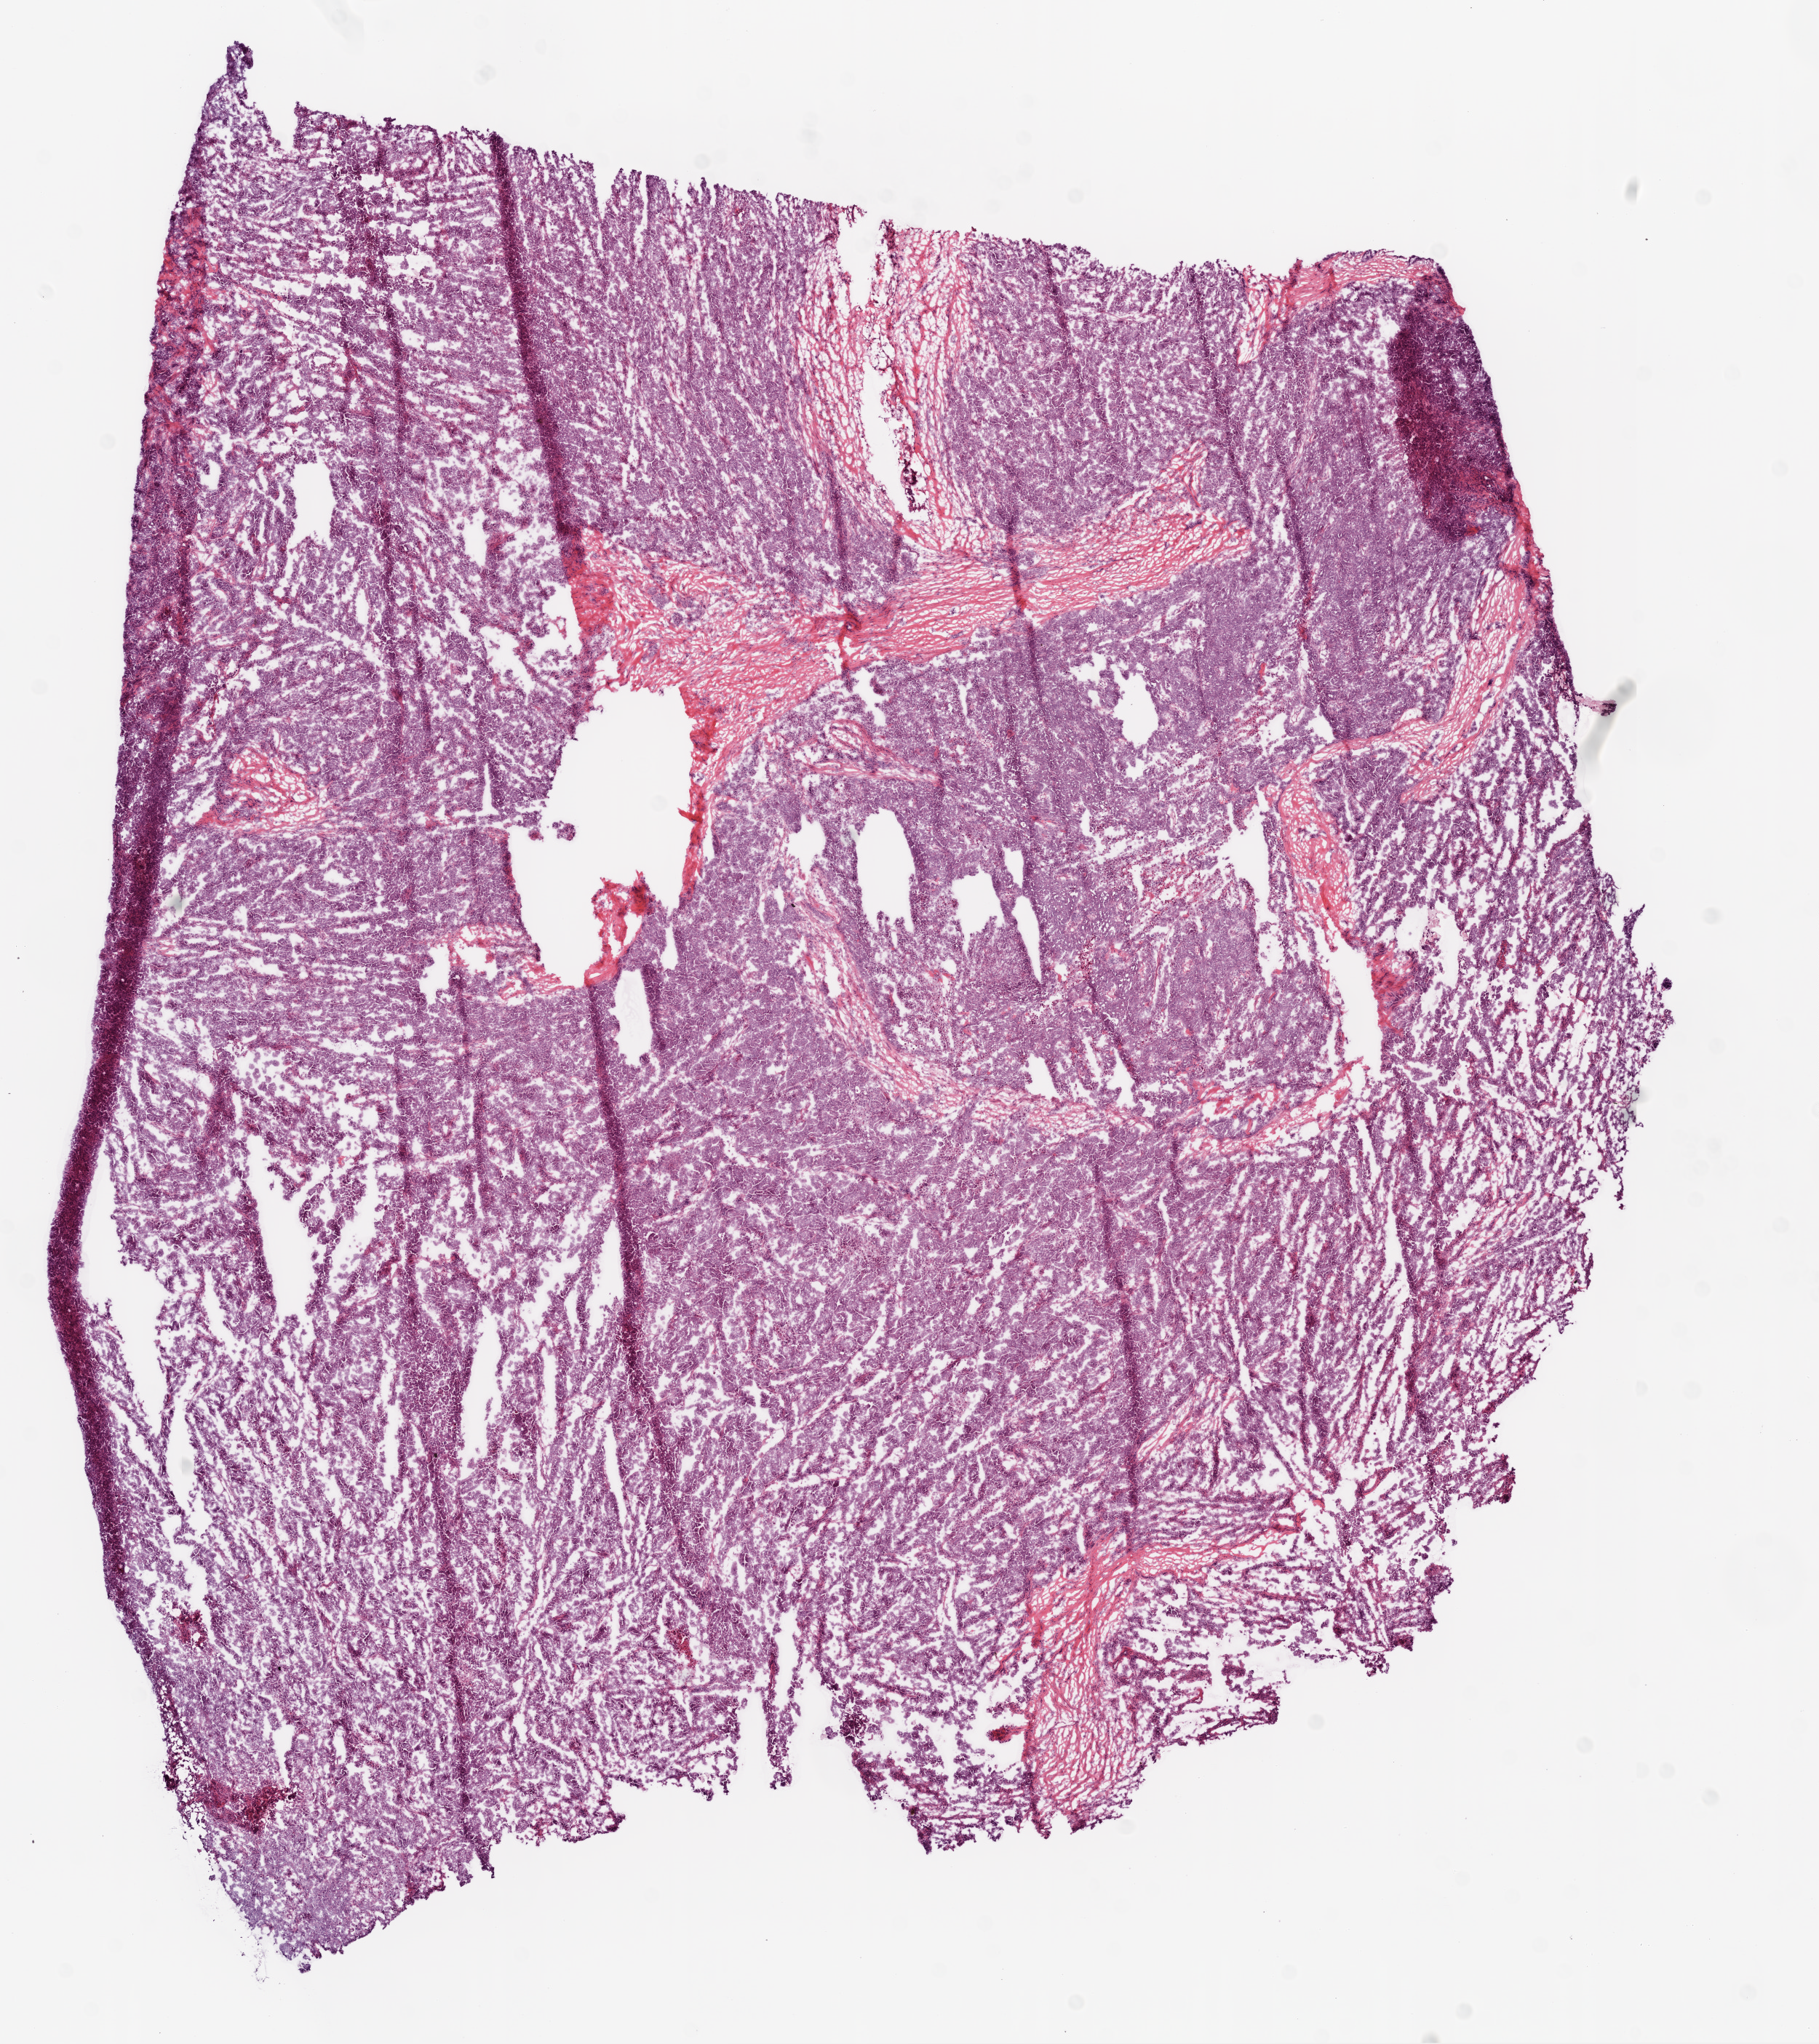
H&E-stained whole-slide image, low-resolution overview of the scanned area, about 10.0 x 11.3 mm. Frozen section from the bottom of the tissue portion. Sample: primary tumour, ovary. Female, age 53 years at initial diagnosis. Histologic grade: G3 (poorly differentiated). Composition of this section per pathologist review: tumour cells 90%, tumour nuclei 90%, normal cells 0%, stromal cells 10%, necrosis 0%. Inflammatory infiltration, as recorded: lymphocyte infiltration 0%, monocyte infiltration 0%, neutrophil infiltration 0%.
Laterality: bilateral. Diagnosis: Serous cystadenocarcinoma, NOS. FIGO stage: IIIC.